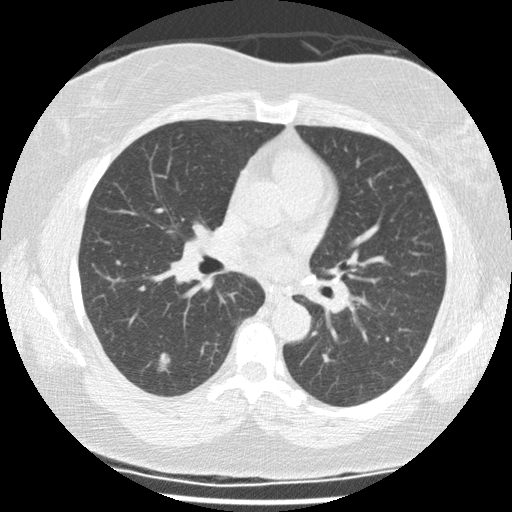
Low-dose screening chest CT, one axial slice. Slice 63 of 117 in the series (ordered by position). 120 kVp. Lung window (W 1500 / L -600 HU). 2.5 mm slice thickness. 512 × 512 image matrix, field of view 325 × 325 mm.
Outlined on this slice (expert manual segmentation):
- lesion 1 (tumor, lower lobe of right lung): bounding box [x1, y1, x2, y2] px = [158, 353, 170, 373]